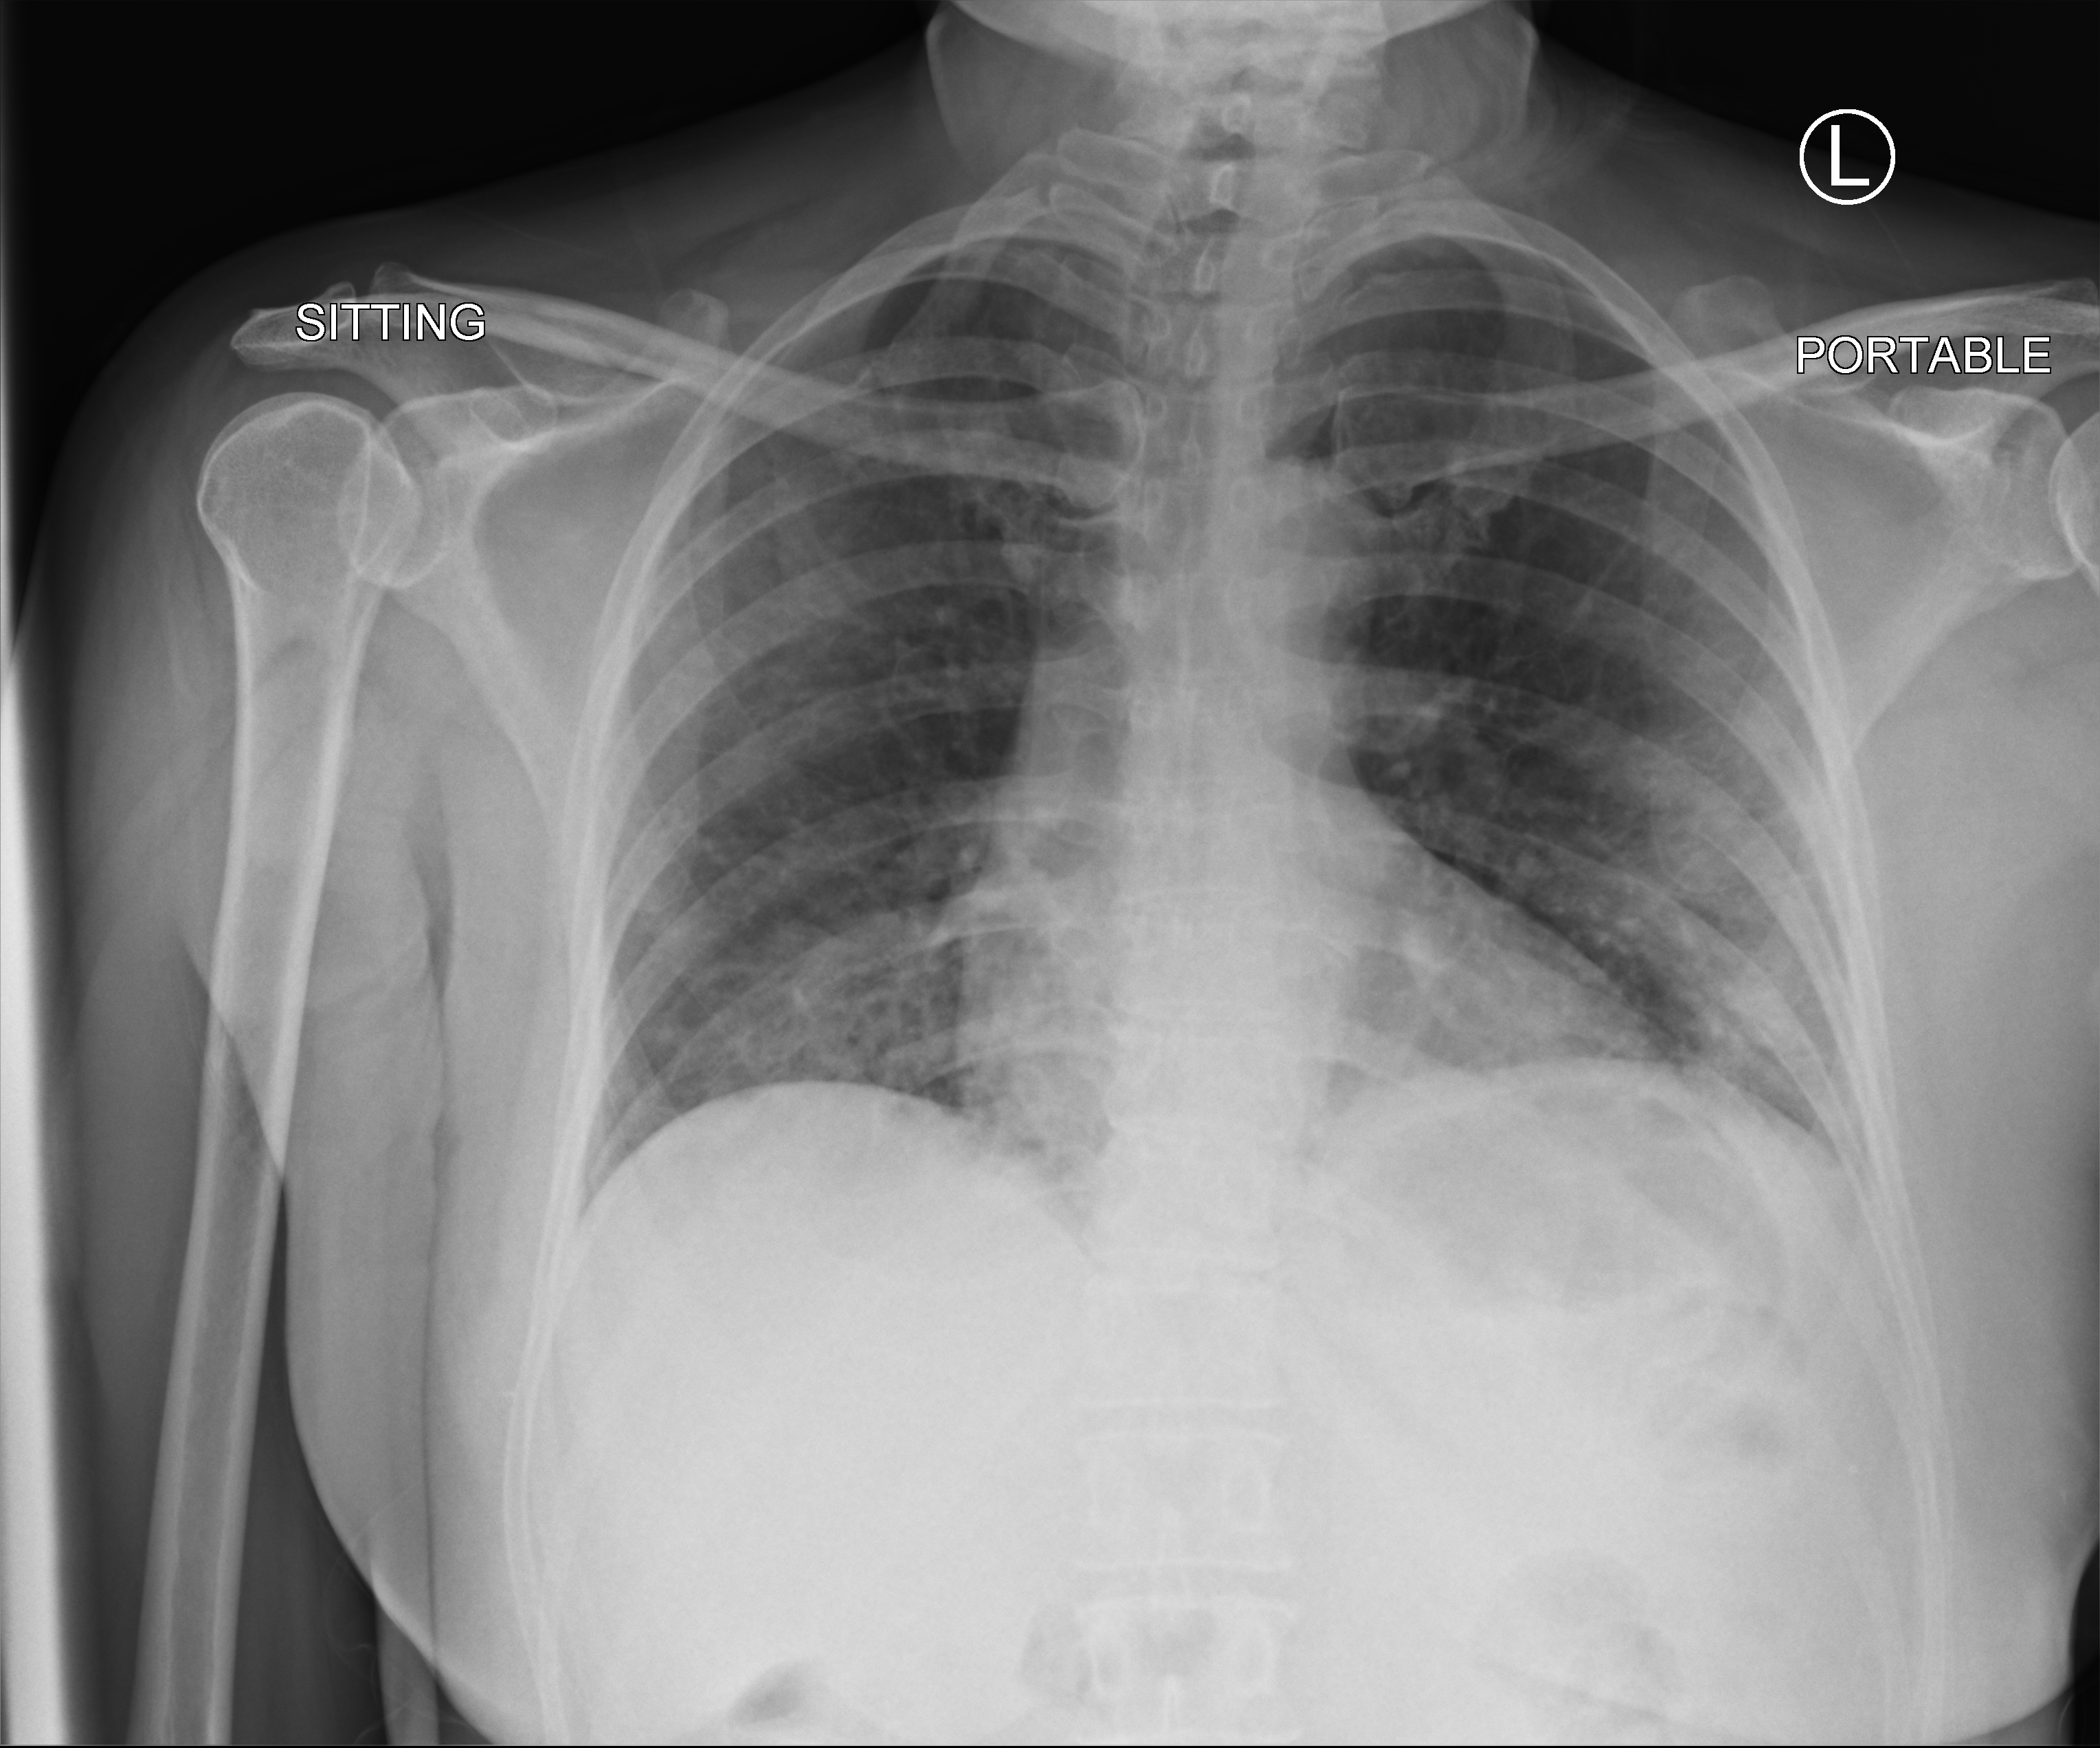
Portable chest radiograph; anteroposterior (AP) projection. Female patient hospitalised with COVID-19, age 18–59 years.
Admission-level facts for this patient (not findings on this image; timing relative to this image not recorded): admitted to intensive care during this hospital stay: no; diabetes (admission record): no; mechanically ventilated during this hospital stay: no.